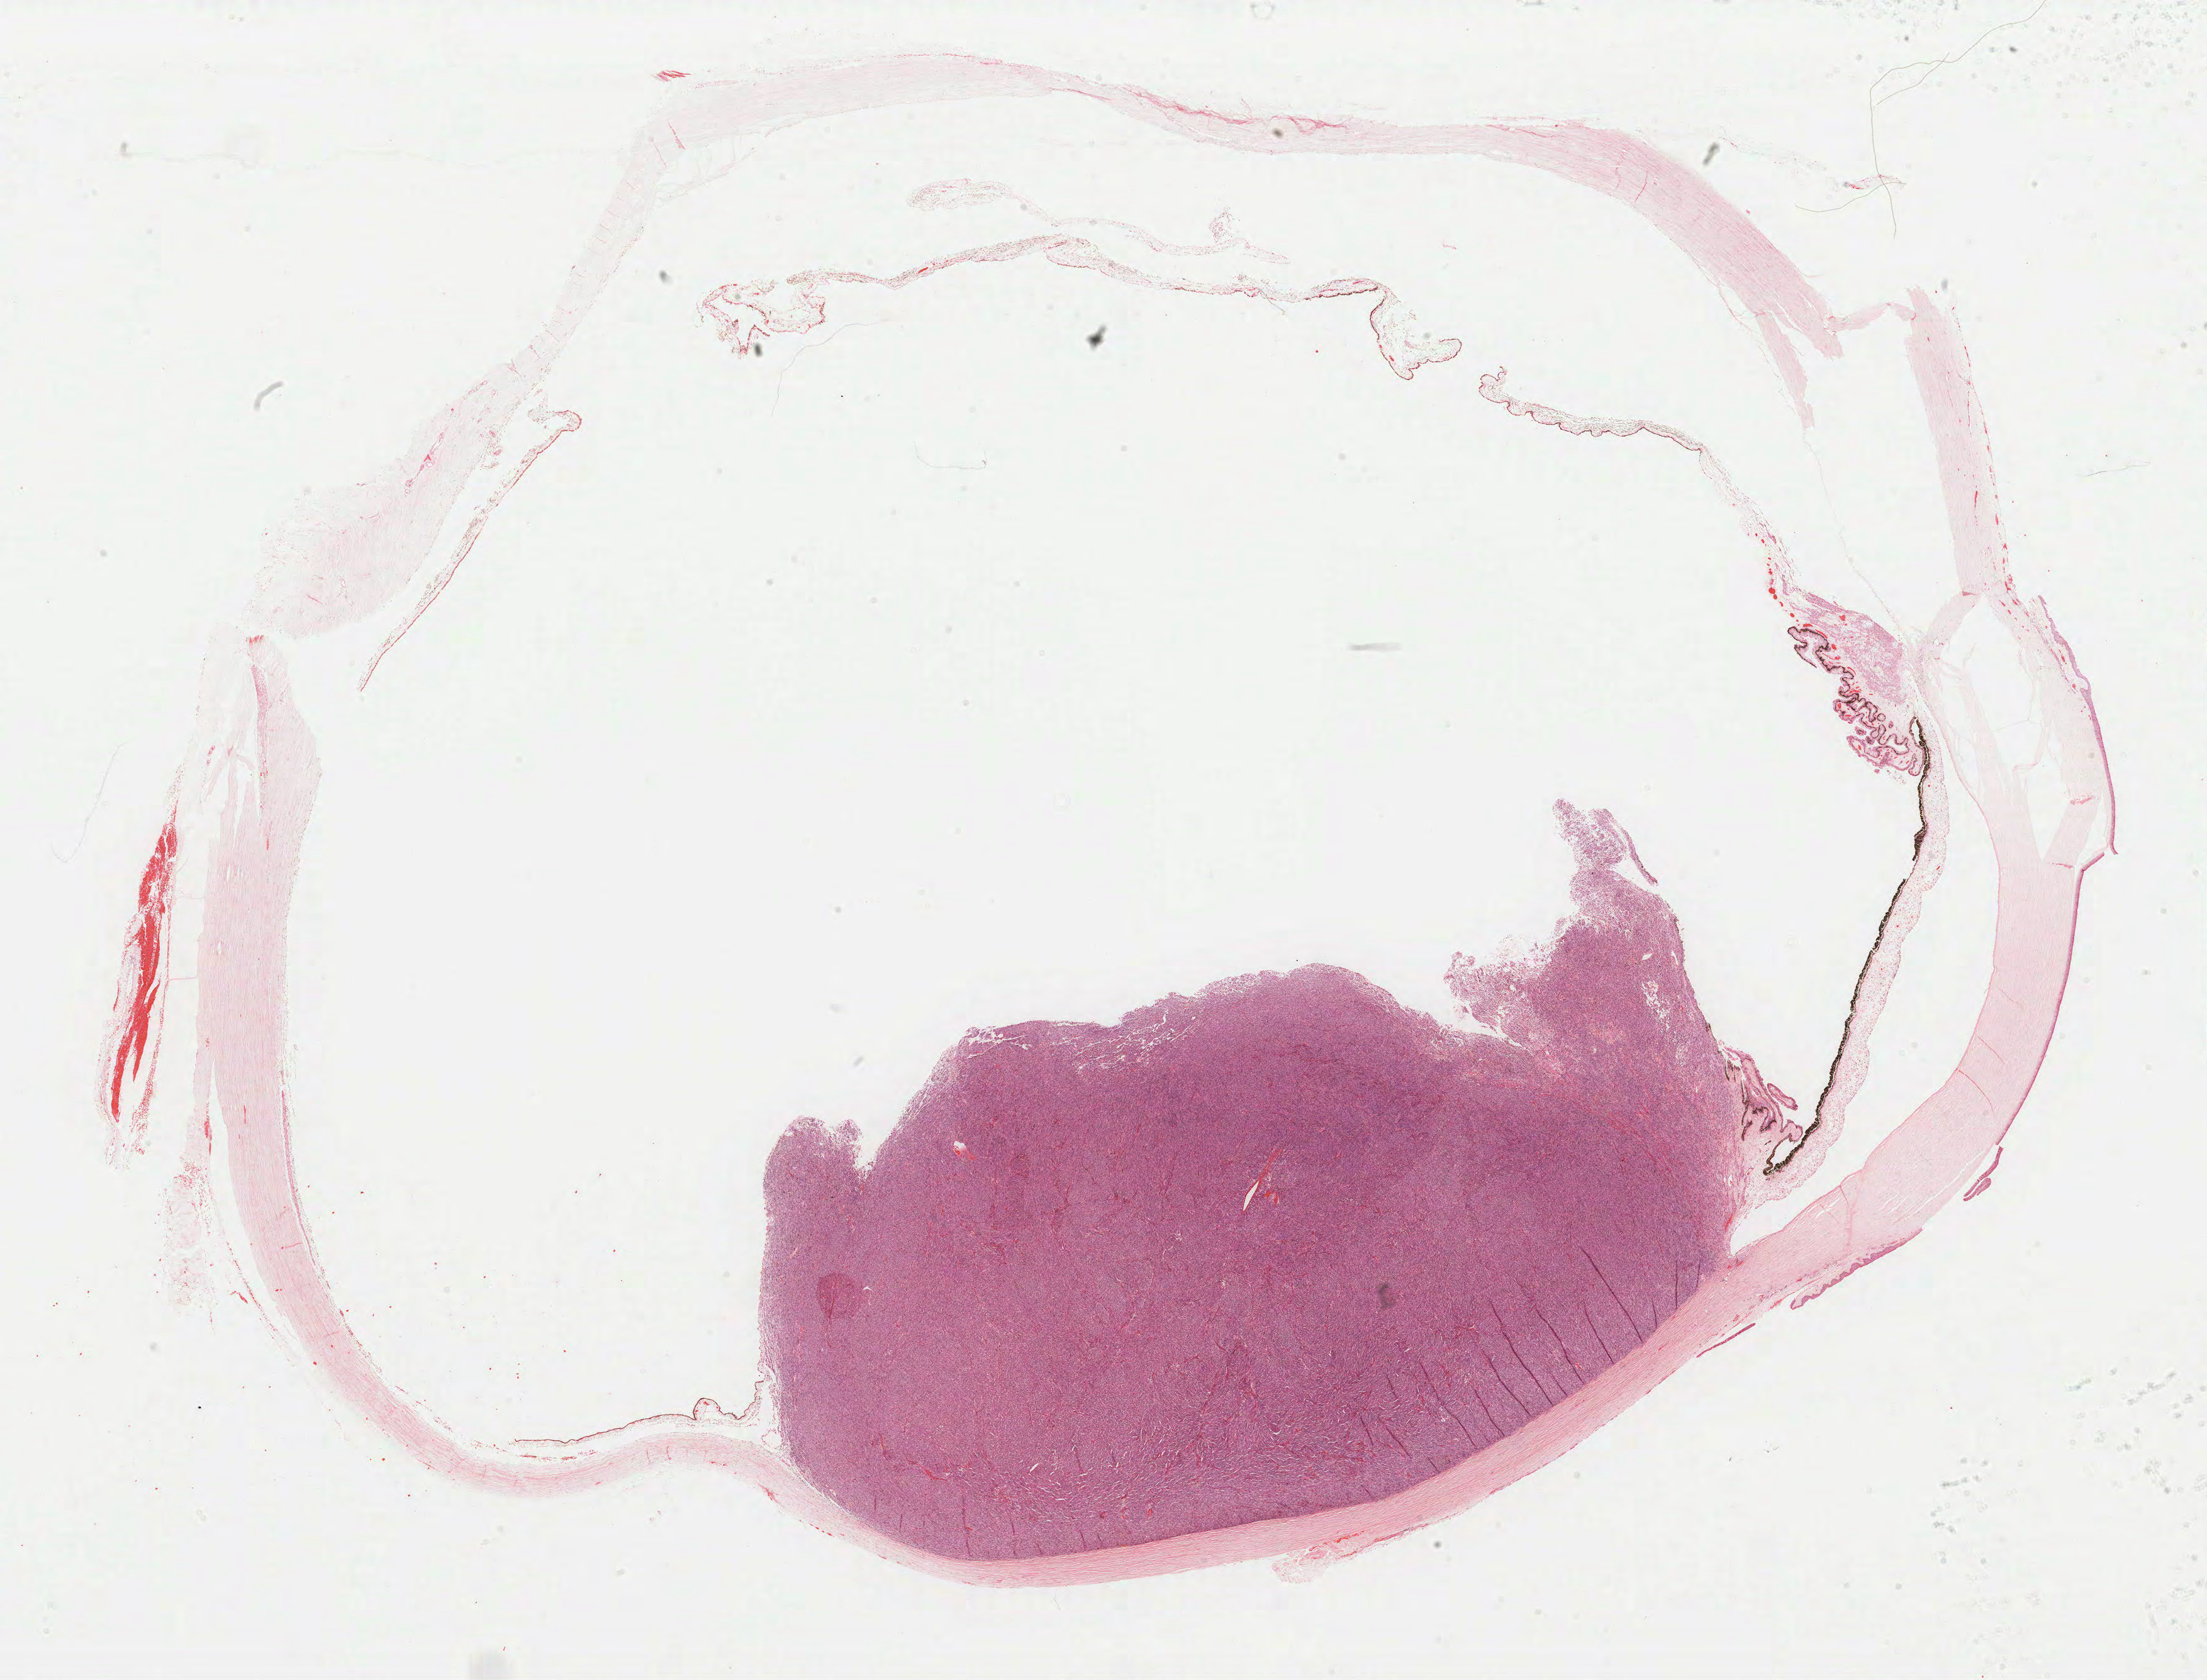
Digitized Hematoxylin and eosin (H&E) stained tissue section (whole slide) — low-resolution overview of the scanned area, about 27.7 x 21.1 mm, FFPE section, sample: primary tumour, uvea. Male patient; age at initial diagnosis 75 years.
Pathologic diagnosis: Mixed epithelioid and spindle cell melanoma (choroid).